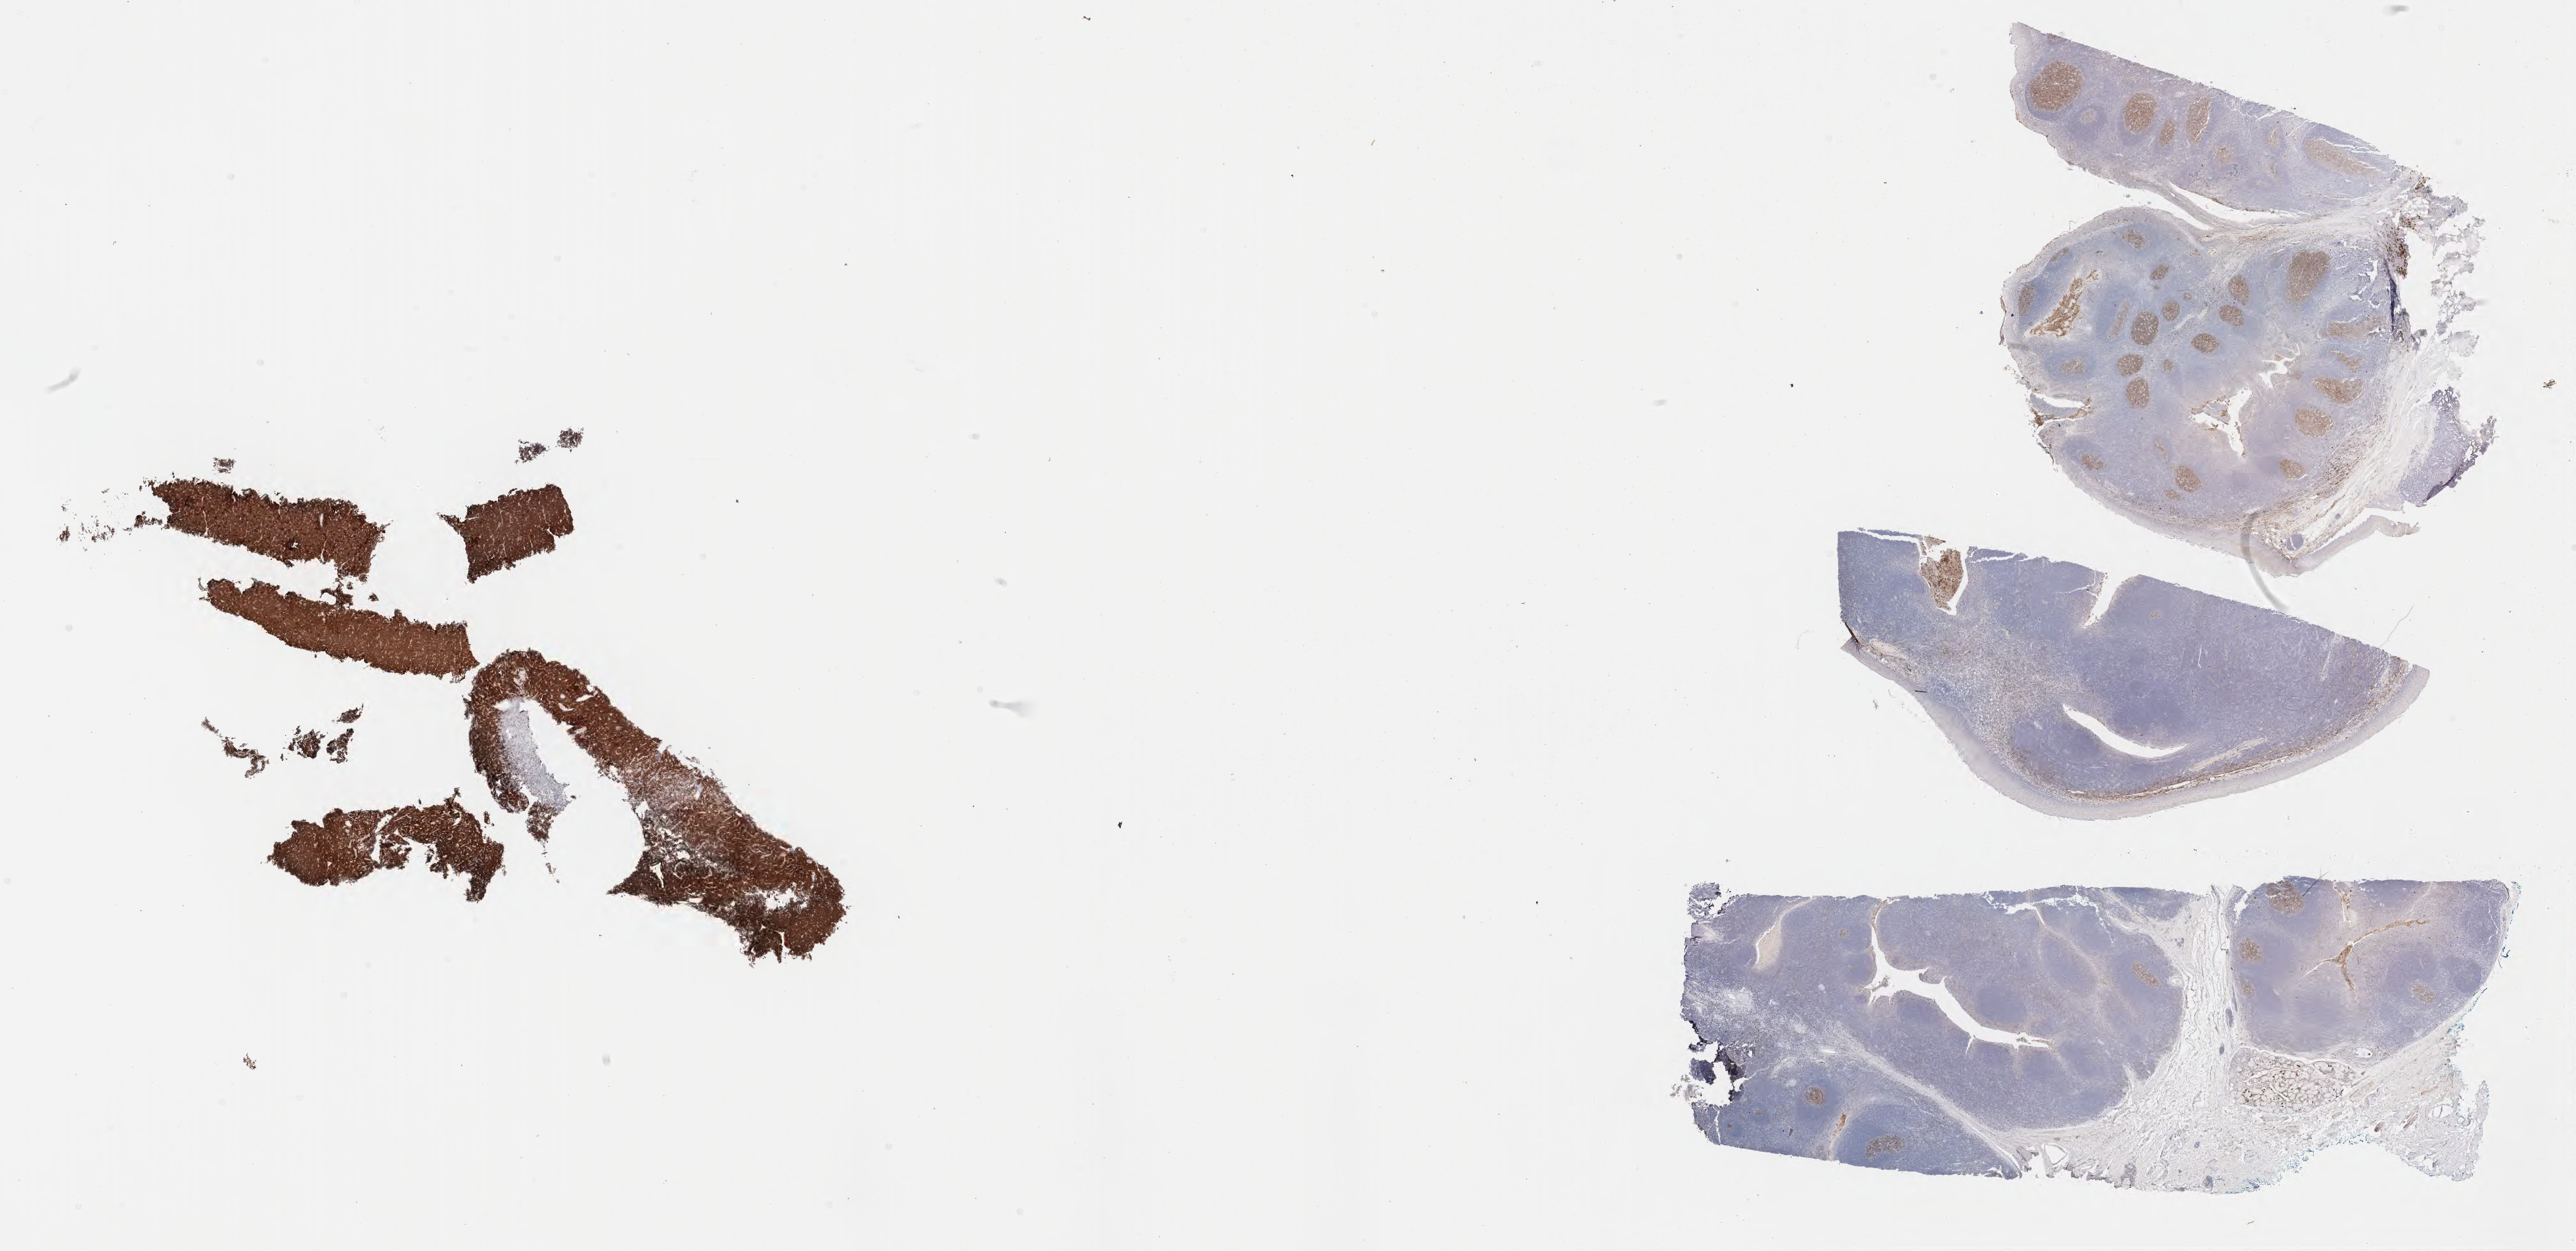
IHC for CD10, whole-slide image, whole scanned area (about 31.7 x 15.4 mm) shown as a low-resolution overview, specimen: tumor tissue, site: liver. Male, age 4 years at initial diagnosis.
Diagnosis: Burkitt lymphoma, NOS.